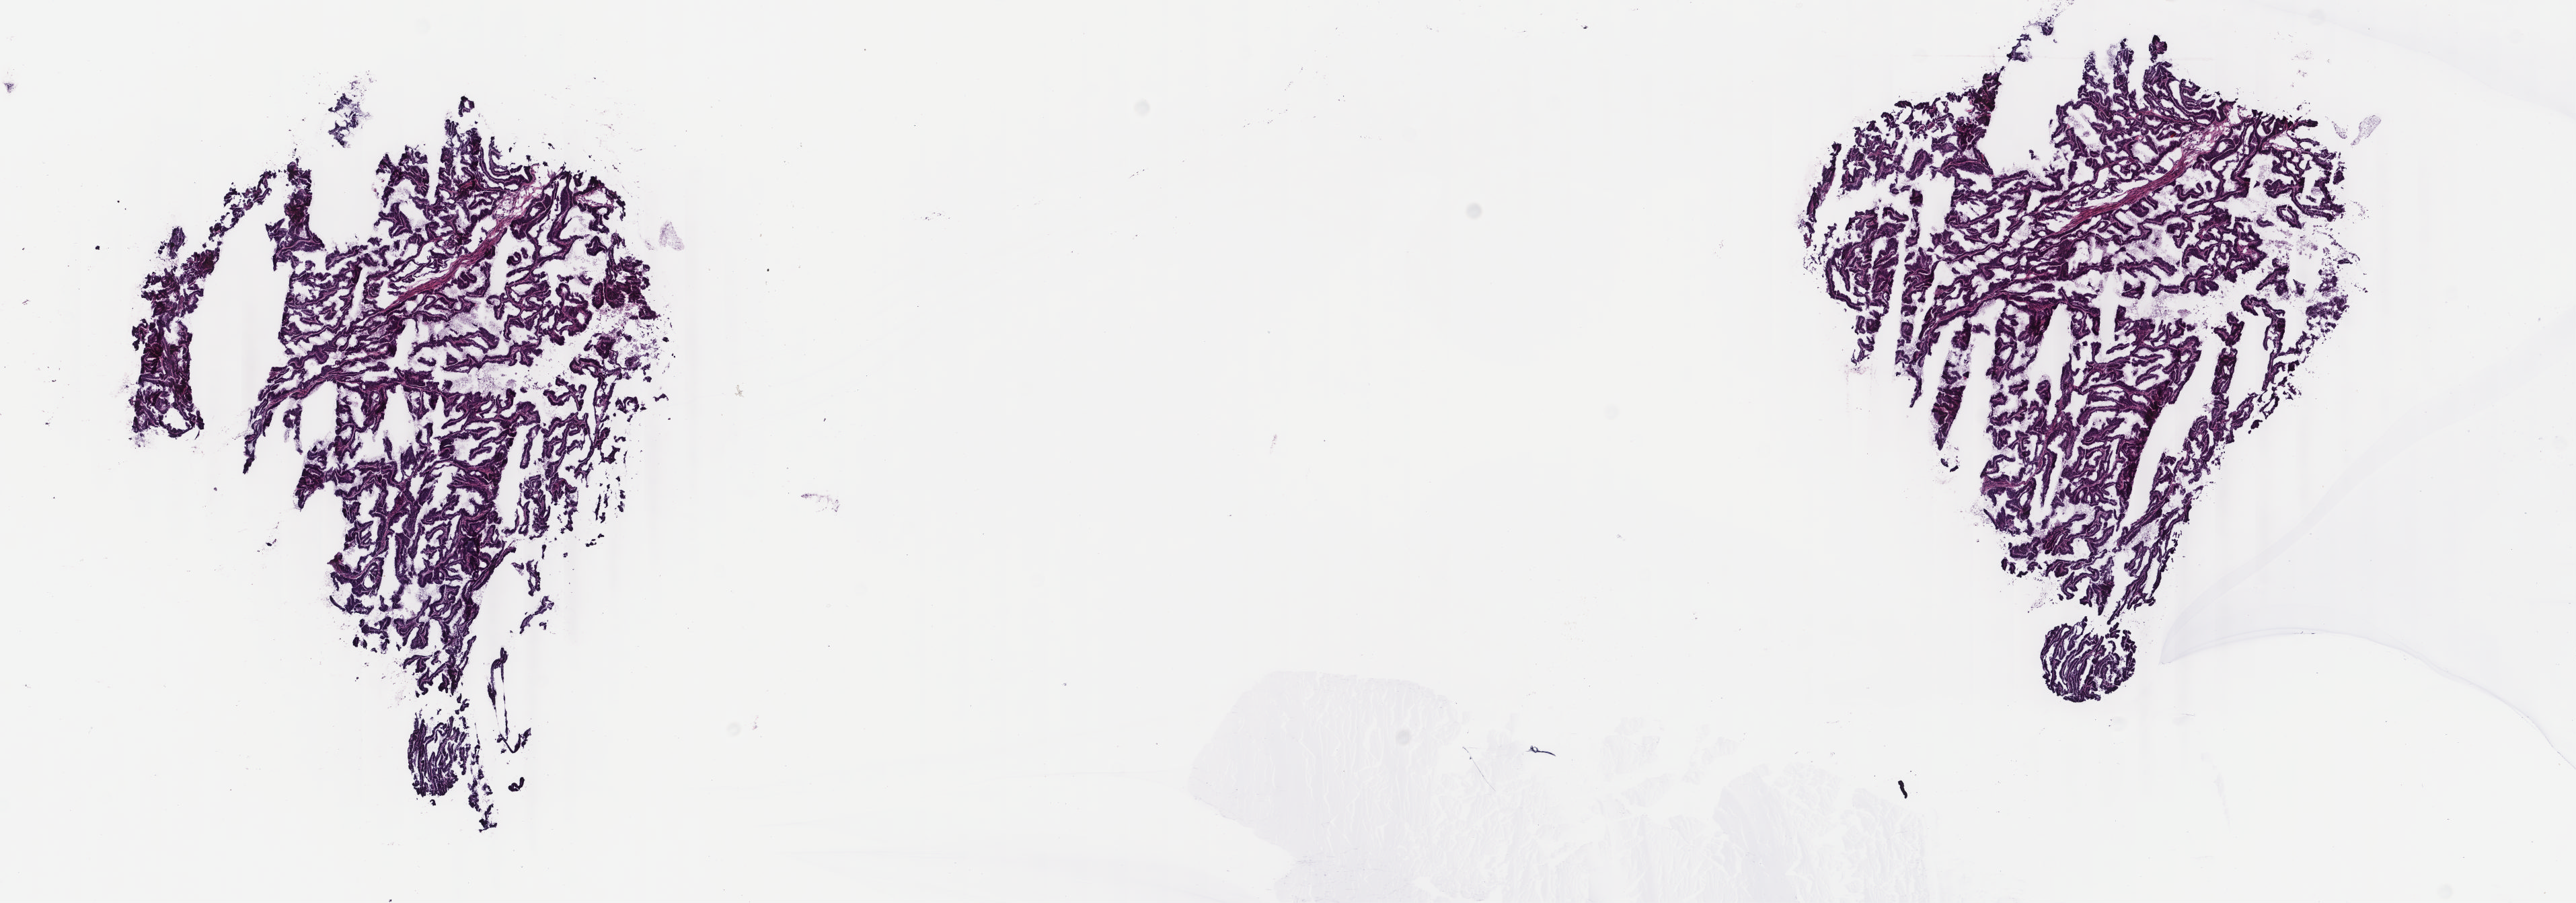
H&E whole-slide image, shown as a low-resolution overview of the whole scanned area (about 15.2 x 5.3 mm, acquisition: 40x scan); frozen section; uterus, primary tumour sample. Female, age 64 years at initial diagnosis. Histologic grade: G1 (well differentiated). Composition of this section per pathologist review: tumour cells 68%, tumour nuclei 70%, normal cells 0%, stromal cells 30%, necrosis 2%. Inflammatory infiltration, as recorded: lymphocyte infiltration 1%, monocyte infiltration 1%, neutrophil infiltration 0%.
Diagnosis: Endometrioid adenocarcinoma, NOS (endometrium). FIGO stage: IIIA.